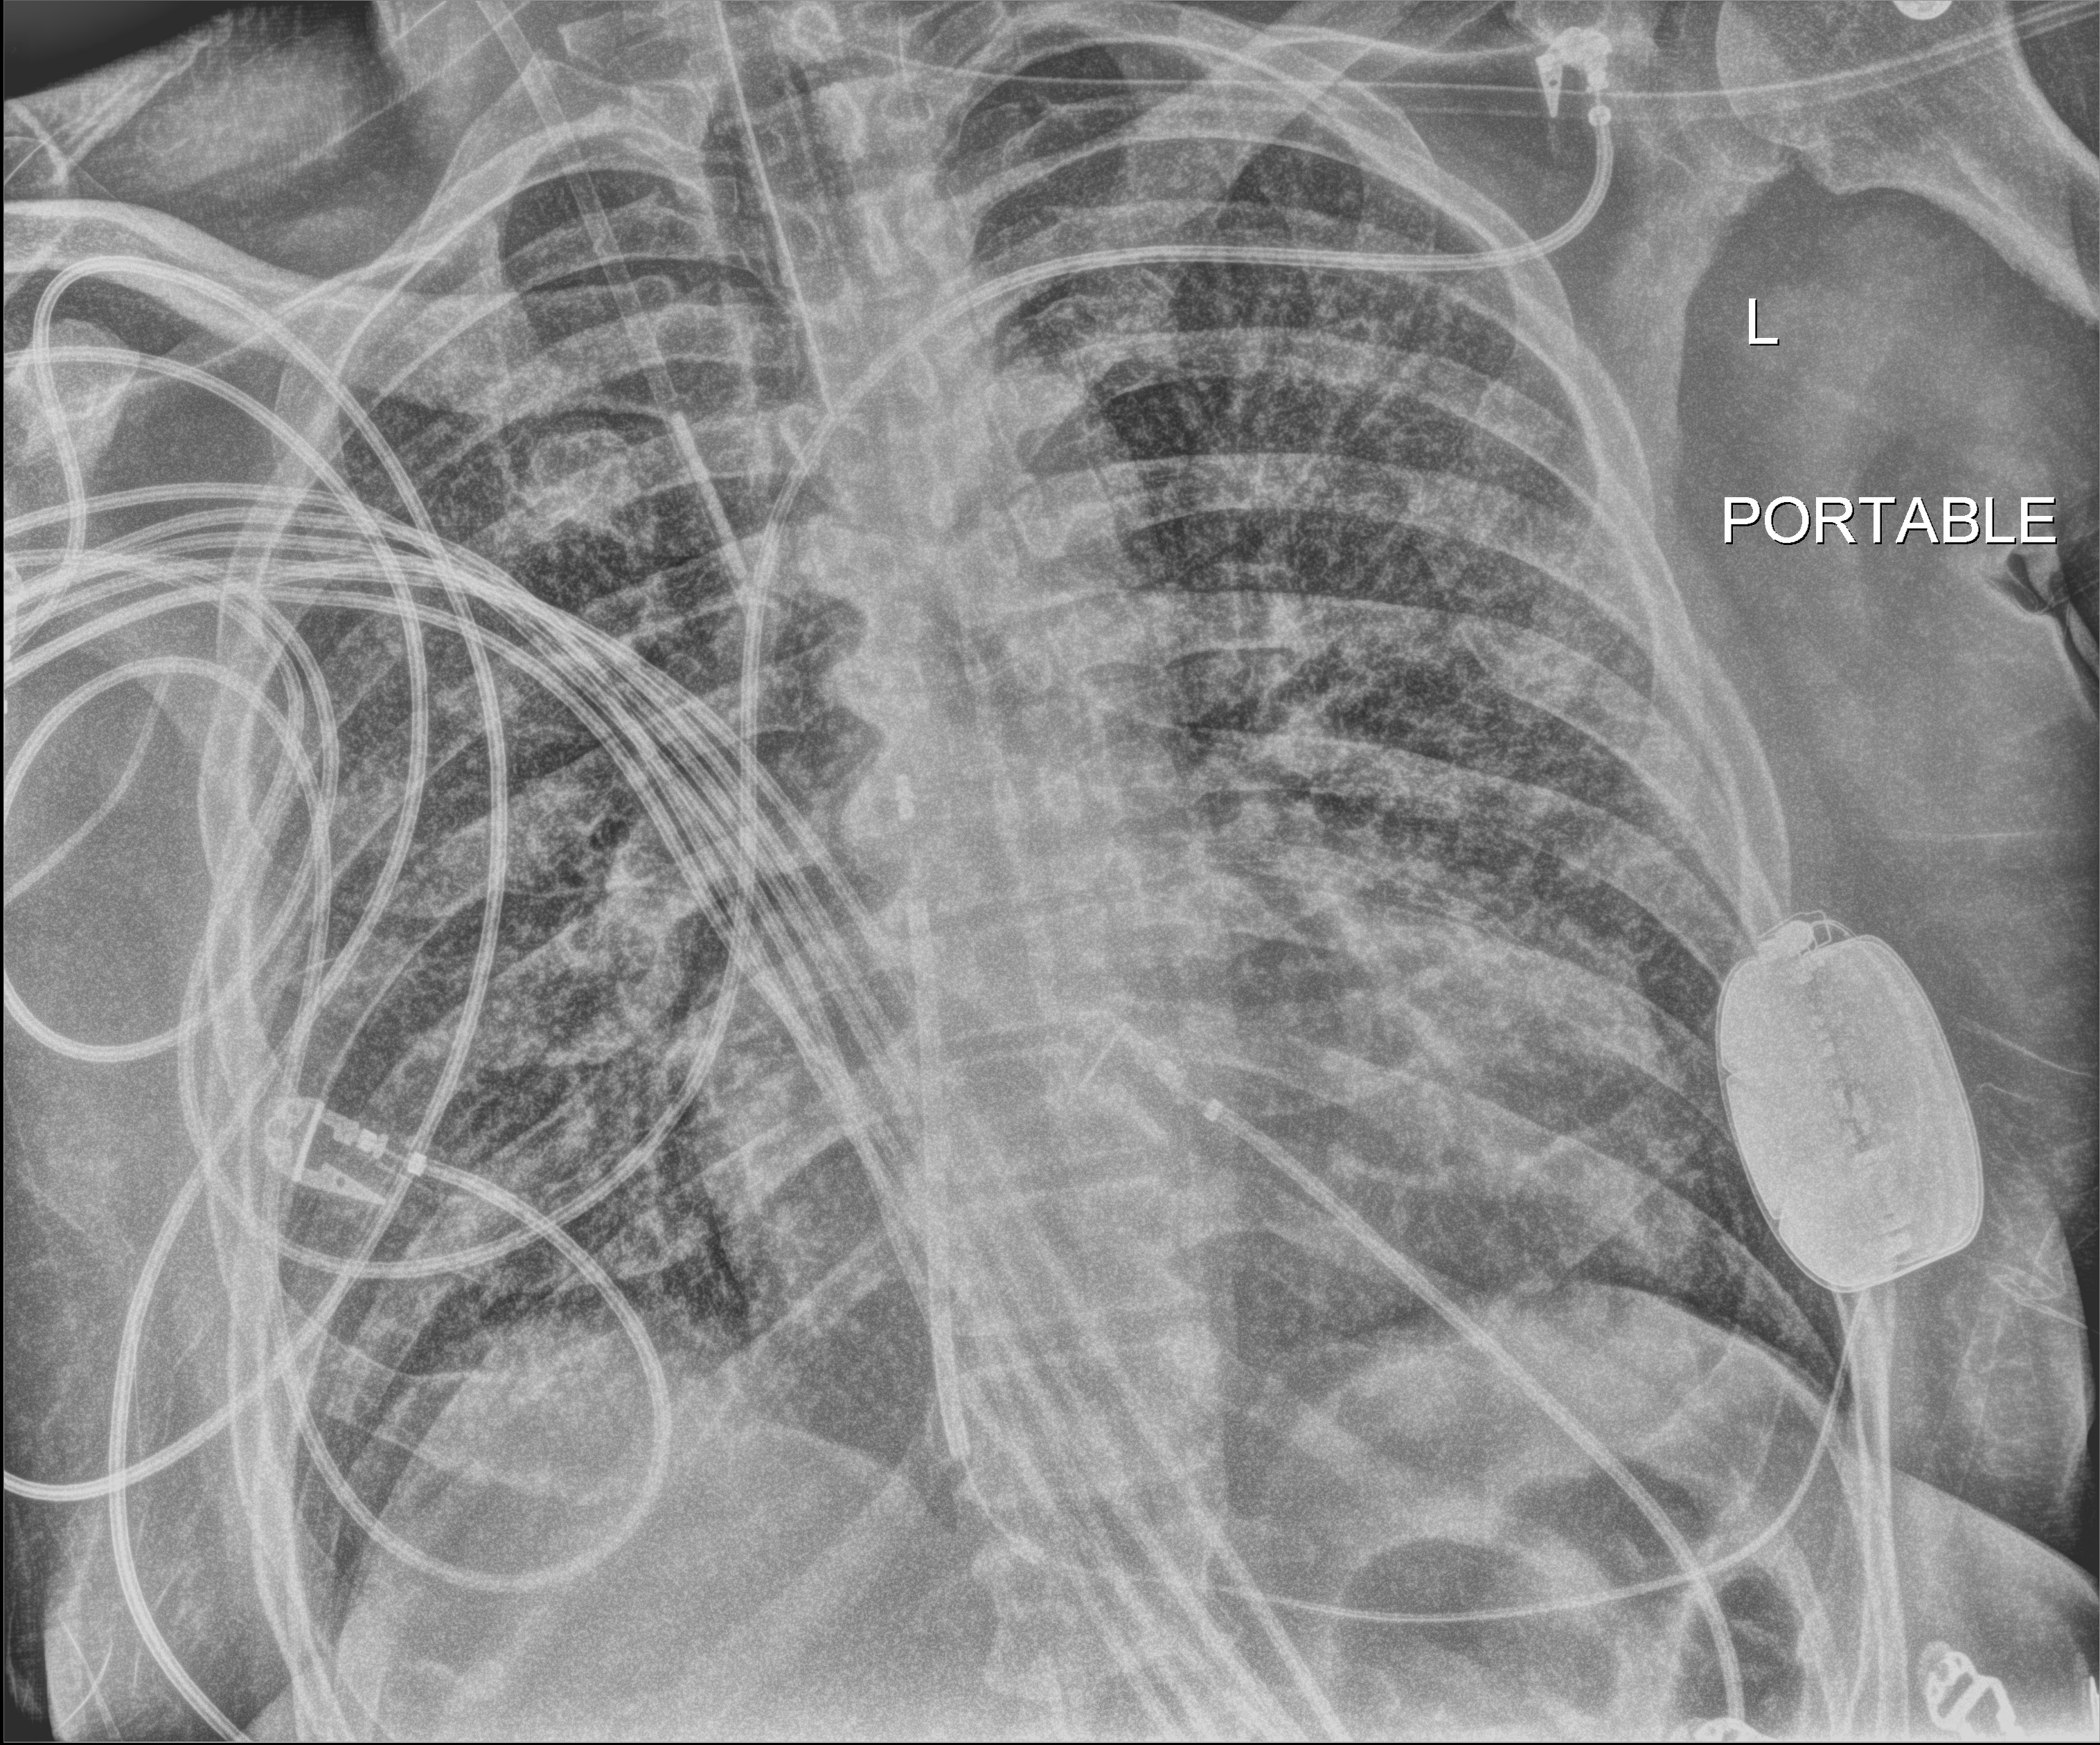
Chest X-ray (portable); anteroposterior (AP) projection. Male patient hospitalised with COVID-19, age 60–74 years.
From the hospital-stay record, not from the radiograph (when in the stay this image was taken is not recorded):
- mechanically ventilated during this hospital stay: yes
- admitted to intensive care during this hospital stay: yes